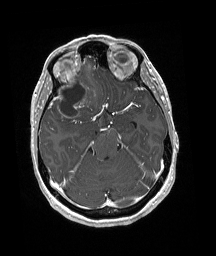
Brain MRI from a brain-tumour surgery series, one axial slice. Slice 121 of 192 in the series (ordered by position). T1-weighted post-contrast. 1 mm slice thickness. 216 × 256 image matrix, field of view 211 × 250 mm. From the clinical record (not read from this slice): histopathology: Oligodendroglioma; WHO grade: 3; IDH mutation: yes.
Structures marked on this image (expert manual segmentation):
- tumour: bounding box <51,74,96,119> (left, top, right, bottom; pixels)